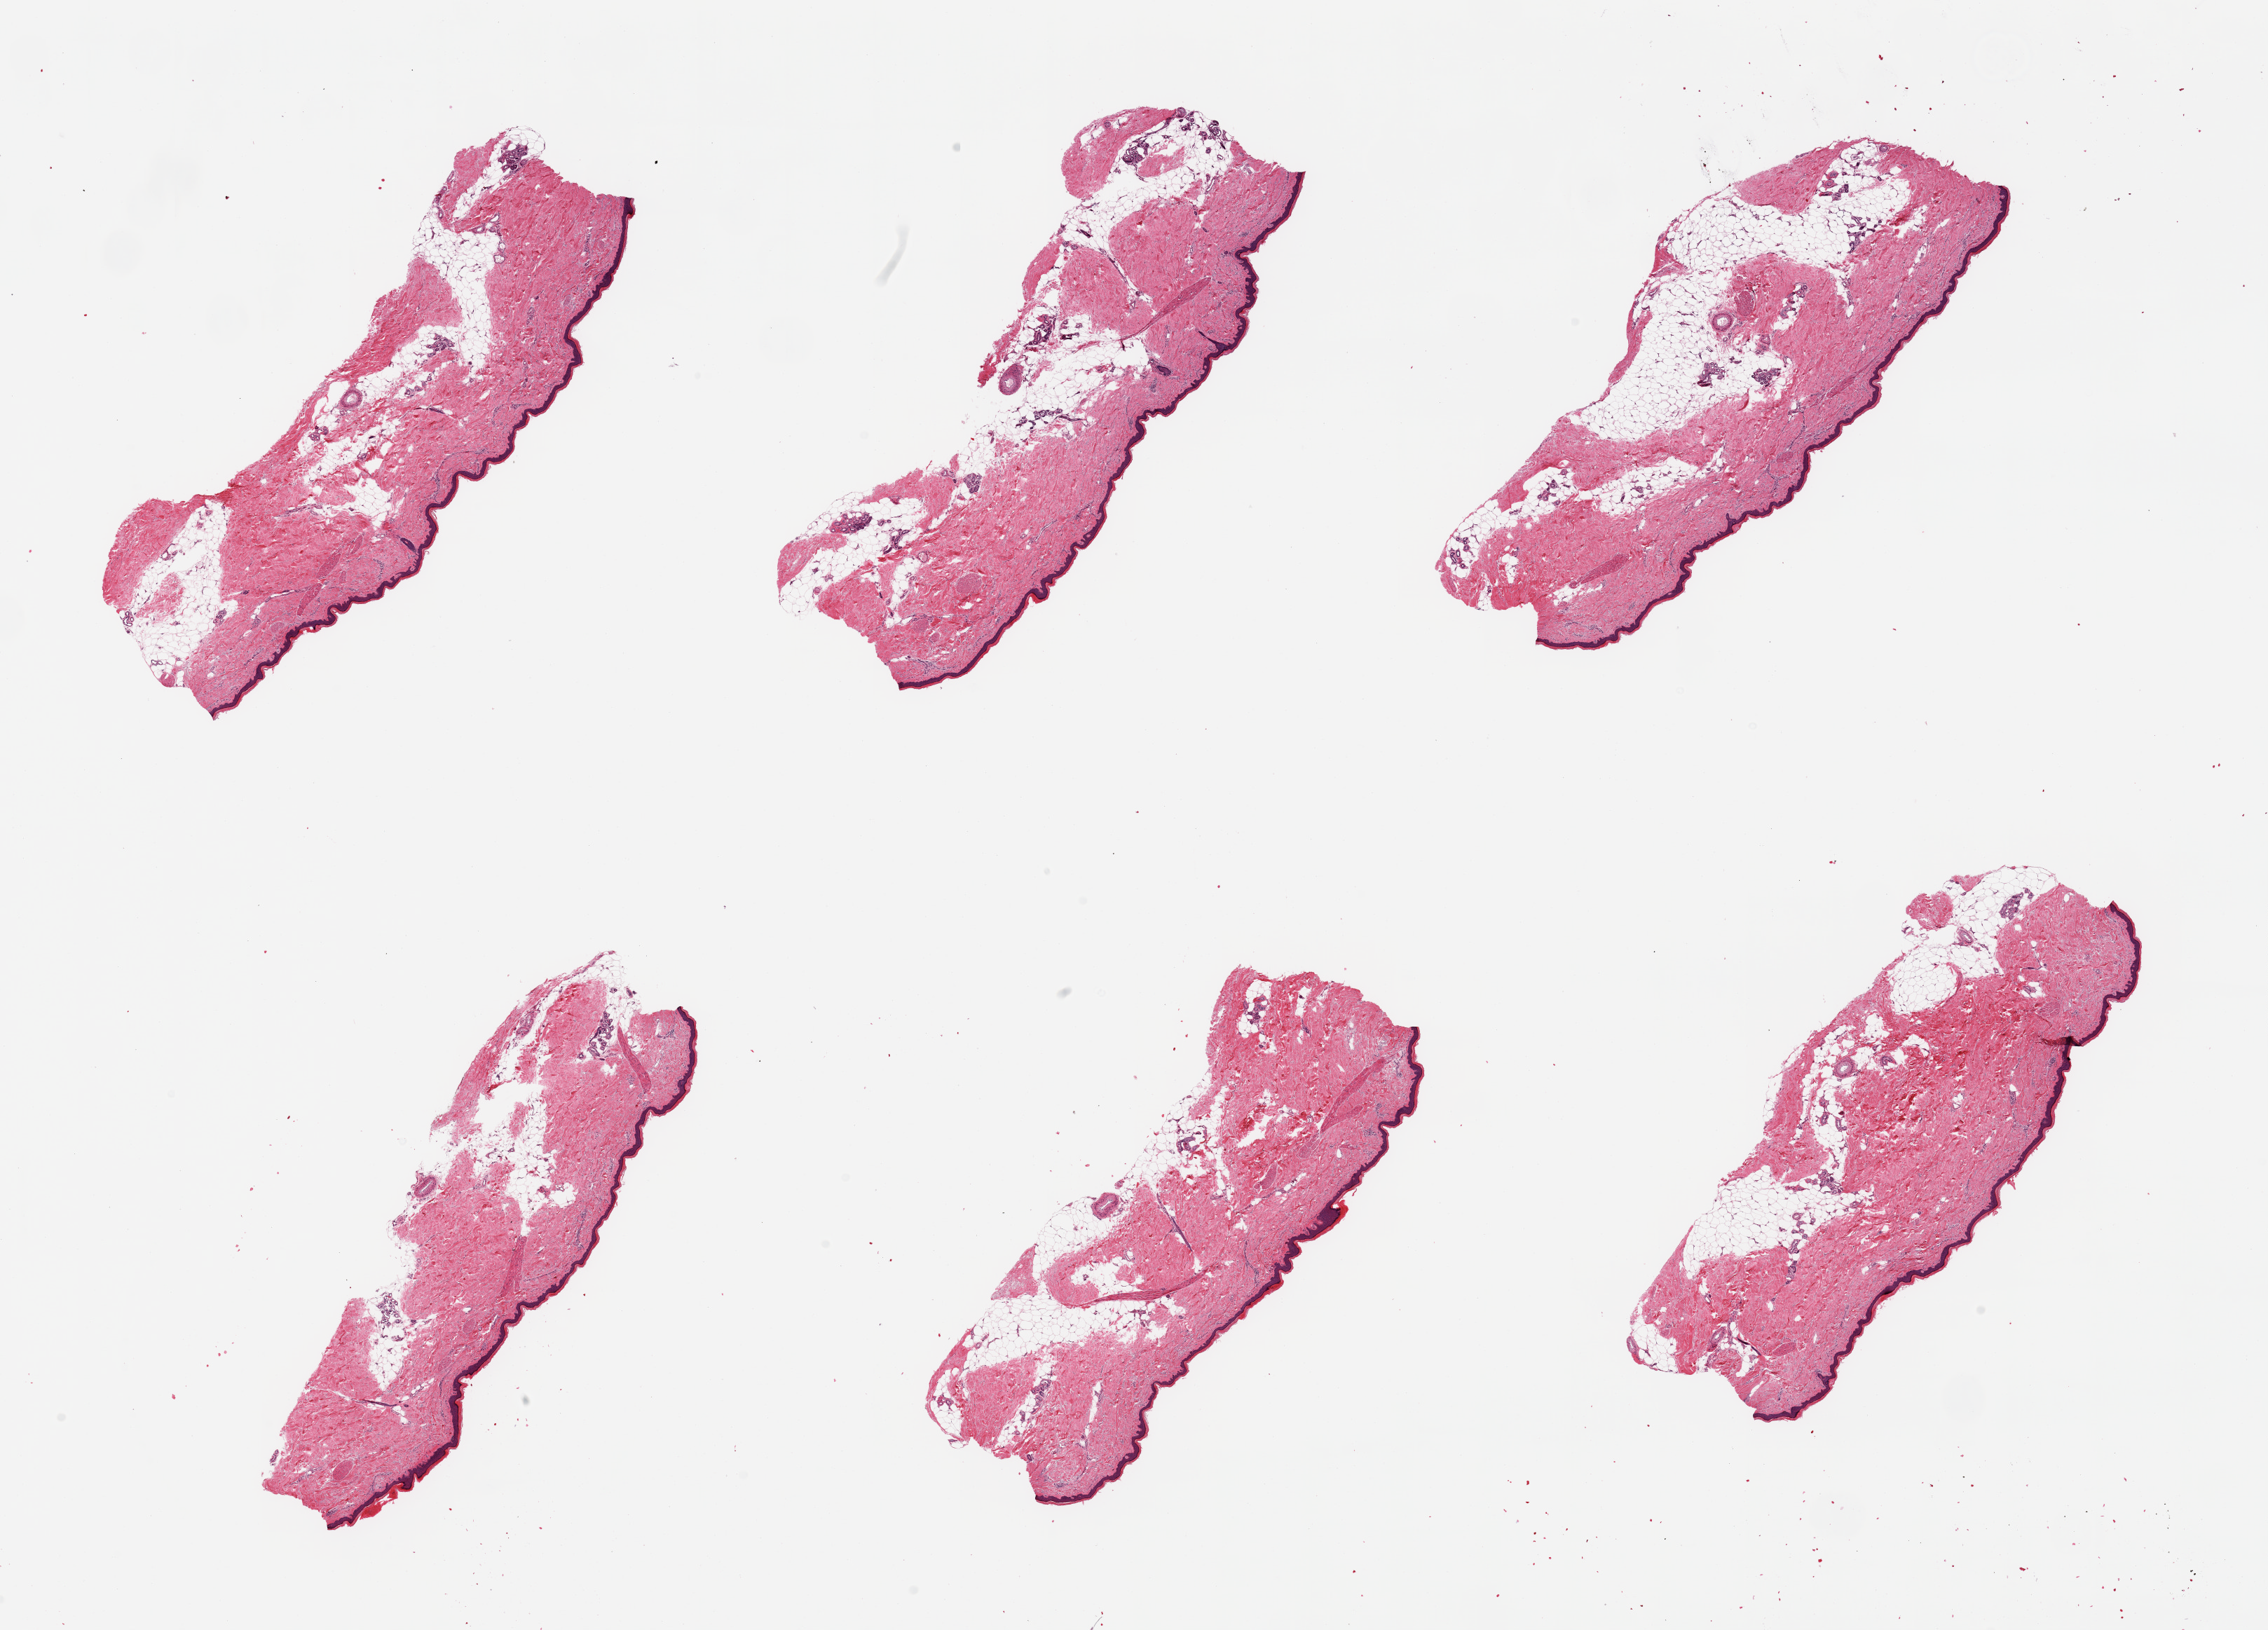
Hematoxylin and eosin (H&E) whole-slide image, low-resolution overview of the scanned area, about 25.6 x 18.4 mm (acquisition: 20x scan). PAXgene-fixed, paraffin-embedded tissue. Target tissue: skin of lower leg. Tissue donor sample.
Reviewer comment on this tissue sample: 6 pieces; well trimmed, but with 30-40% dermal fat.